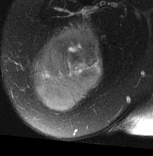
MRI of an extremity soft-tissue mass, one axial slice. Position 27 of 77 along the scan axis. T2-weighted fat-saturated. MR volume resampled by the dataset authors to the PET/CT grid (not the native acquisition matrix). 3.27 mm slice thickness. 153 × 156 image matrix, field of view 149 × 152 mm. Female patient. Case-level facts recorded for this patient, not image findings: histological type: synovial sarcoma; grade: intermediate; site of the primary tumour: right buttock.
Annotated regions visible in this slice (expert contour drawn on MRI and transferred to this co-registered scan by the dataset authors):
- gross tumour volume including surrounding oedema: box from (x=30, y=20) to (x=102, y=112) px
- gross tumour volume (mass): (x=30, y=27)–(x=102, y=112)